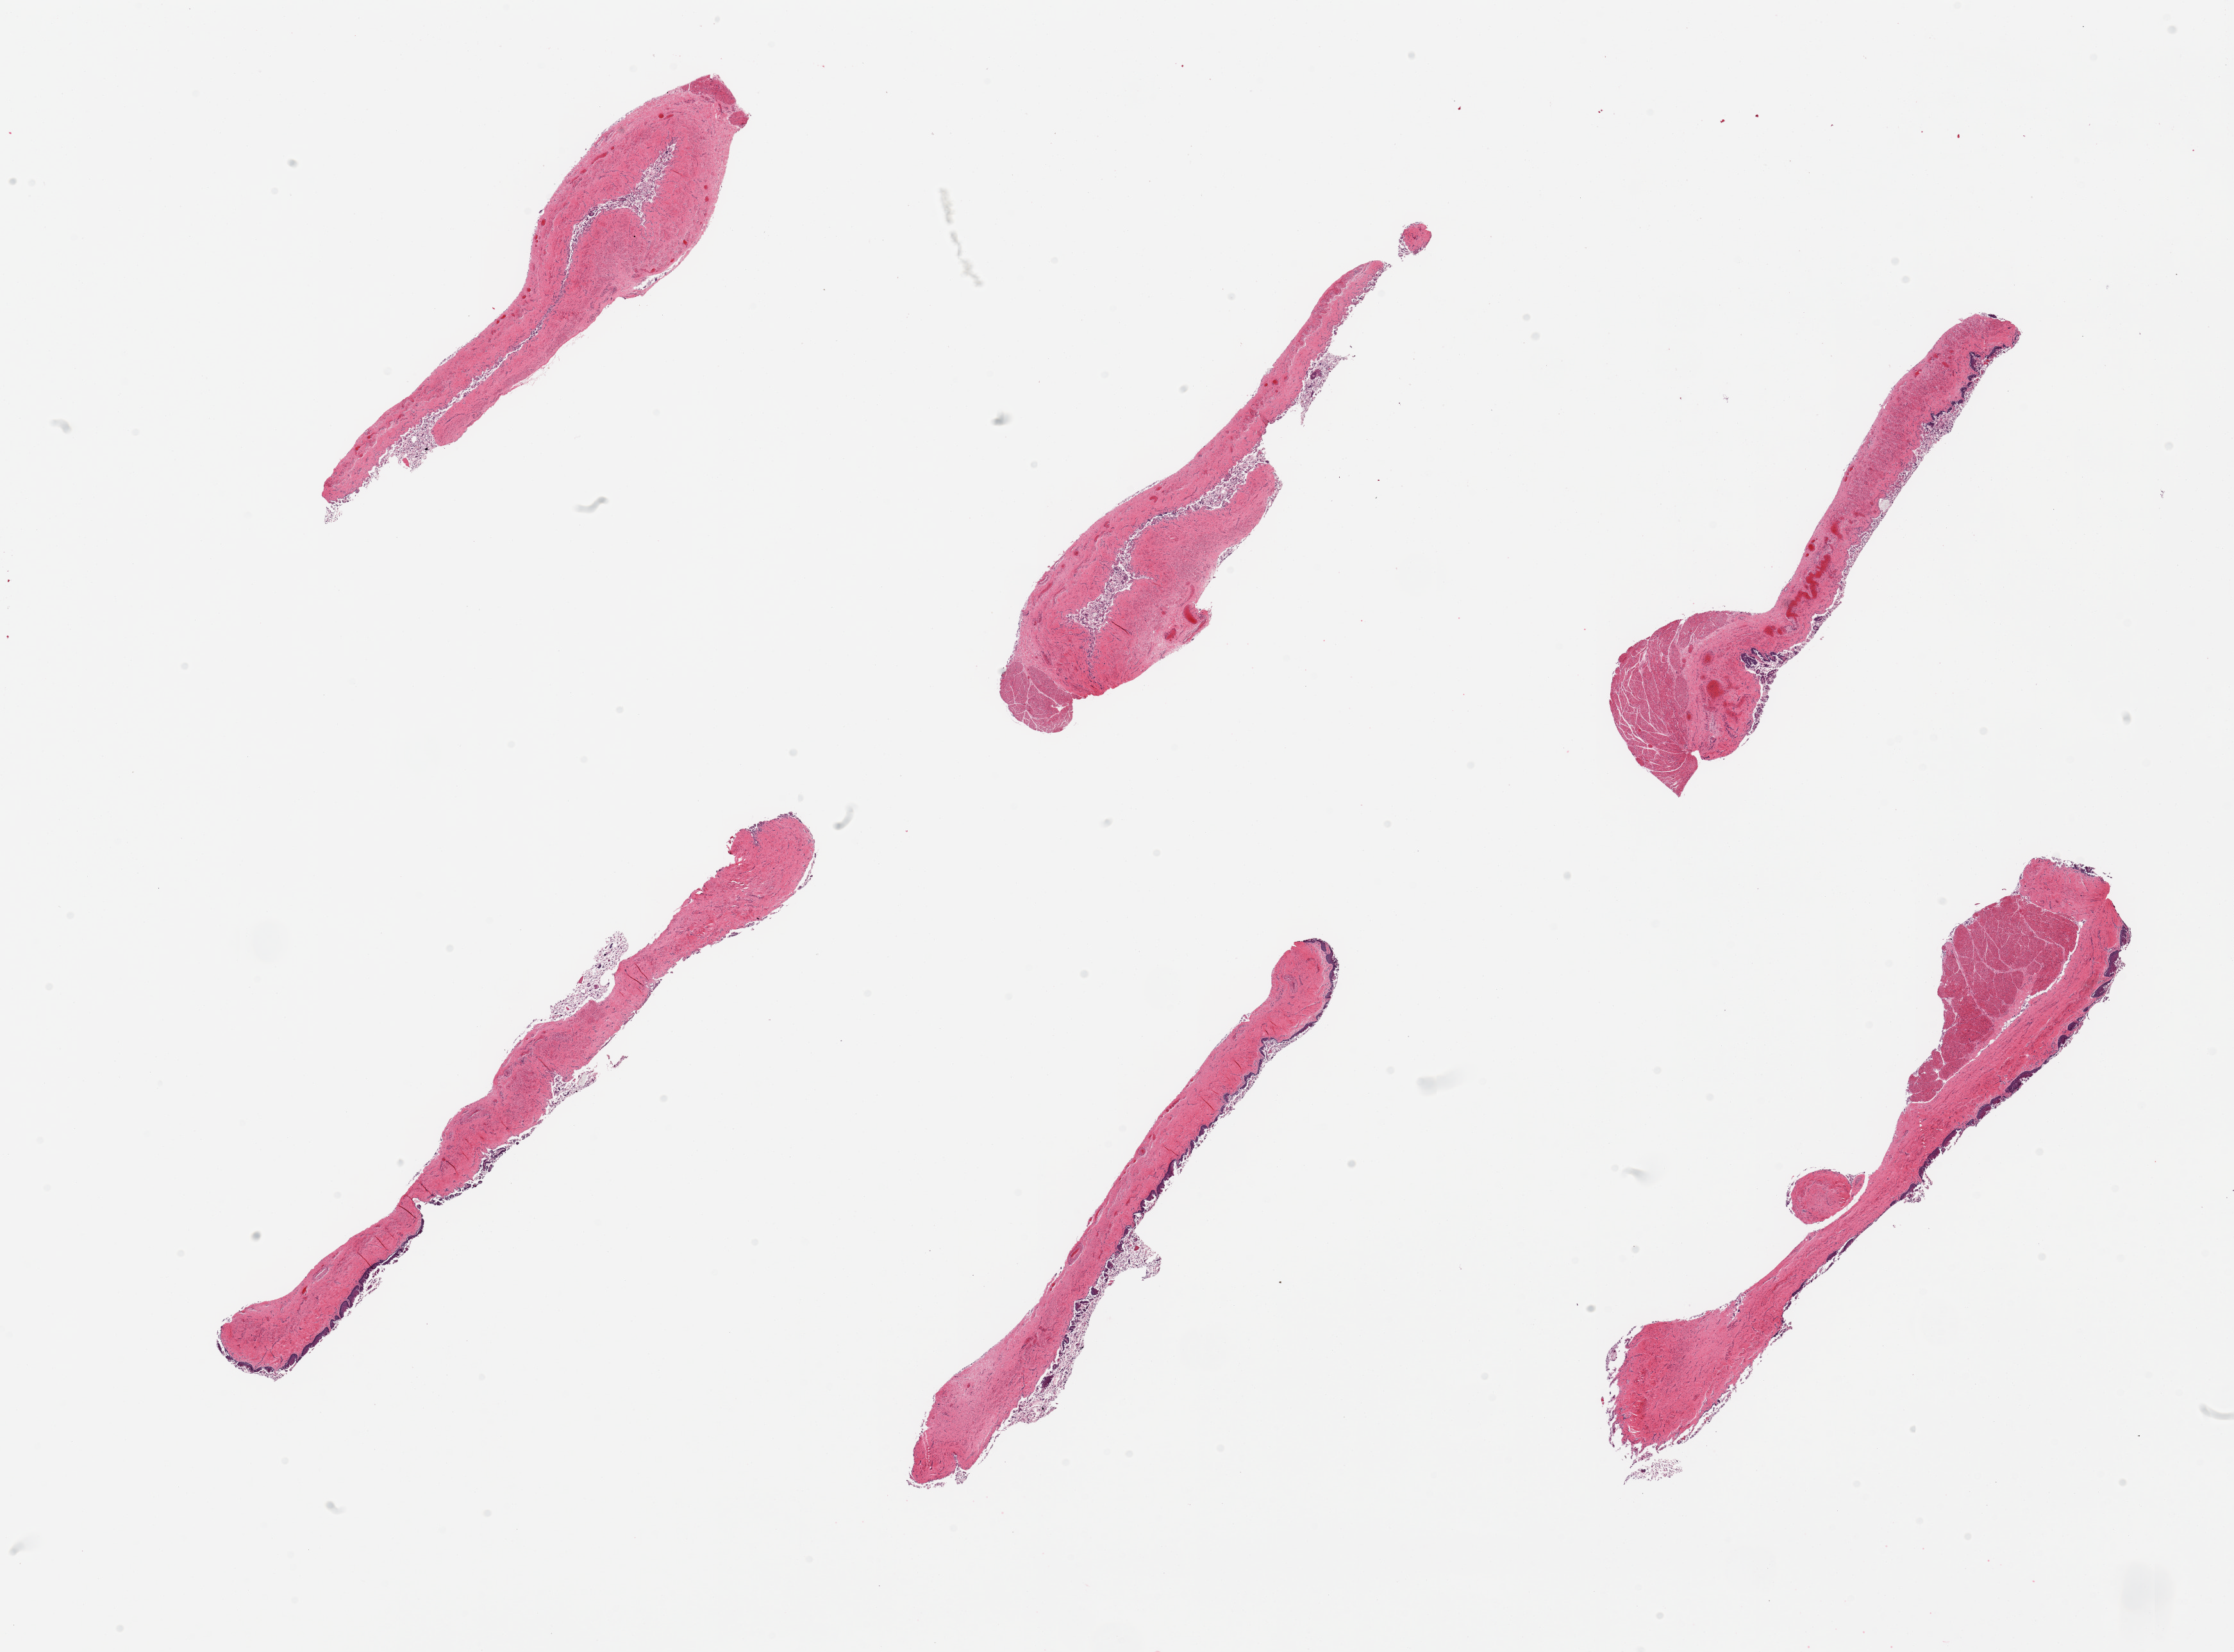
H&E whole-slide image, shown as a low-resolution overview of the whole scanned area (about 27.6 x 20.4 mm), PAXgene-fixed, paraffin-embedded tissue, sampled site (target tissue): esophageal mucous membrane, donor tissue sample. Donor: male.
Pathologist's review note for this sample: 6 pieces, squamous mucosa badly autolyzed, largely sloughed.